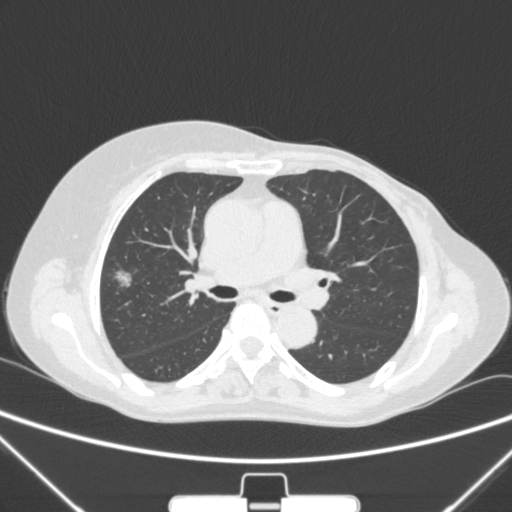
Chest CT, one axial slice; position 154 of 265 along the scan axis; lung window (W 1500 / L -600 HU); 1 mm slice thickness; 512 × 512 image matrix, field of view 350 × 350 mm. Patient: female, 64 years. From the clinical record (not read from this slice): clinical TNM (as recorded): T1c N0 M0; histopathological grade: G1-2.
Outlined on this slice (bounding box drawn by a radiologist):
- lung tumour (recorded histology: adenocarcinoma): bounding box [x1, y1, x2, y2] px = [102, 261, 141, 290]